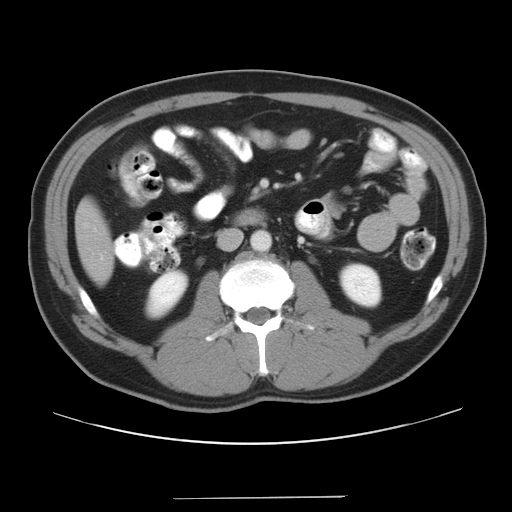
Contrast-enhanced abdominal CT, one axial slice; 120 kVp; intravenous contrast given; soft-tissue window (W 400 / L 40 HU); 512 × 512 image matrix, field of view 400 × 400 mm. Male patient, age 46 years. Case-level facts recorded for this patient, not image findings: diagnosis: colorectal cancer liver metastases, imaged before liver resection; multiple liver metastases: yes.
Annotated regions visible in this slice (manually delineated by an expert):
- liver: bounding box (x1, y1, x2, y2) in pixels: (79, 205, 112, 281)
- planned liver remnant (the part of the liver to remain after resection): (79, 205, 112, 281)